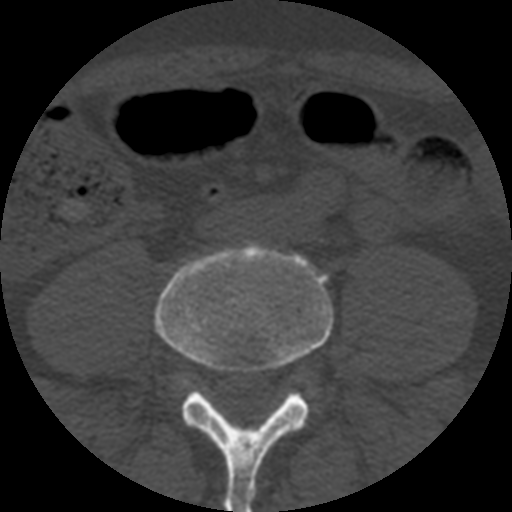
CT including the spine, one axial slice. Position 84 of 508 along the scan axis. Reconstruction kernel STANDARD. Bone window (W 1800 / L 400 HU). 512 × 512 image matrix. Patient age 57 years. From the clinical record (not read from this slice): primary cancer: prostate.
Annotated regions visible in this slice (semi-automatically segmented with operator editing):
- L4 vertebra: bounding box (x1, y1, x2, y2) in pixels: (156, 241, 334, 512)
- L5 vertebra: (181, 380, 184, 384)